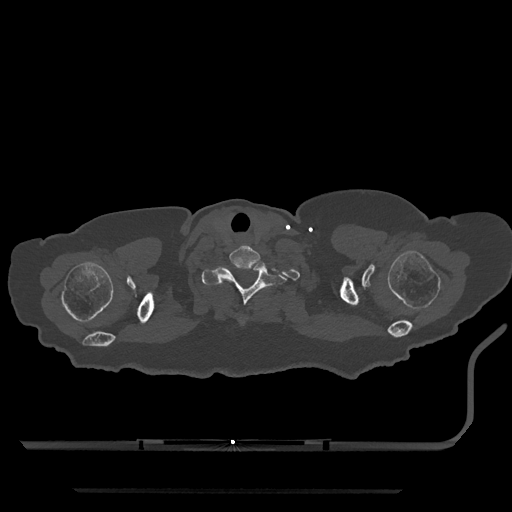
CT including the spine, one axial slice; position 719 of 797 along the scan axis; bone window (W 1800 / L 400 HU); 512 × 512 image matrix. Female patient, age 51 years. From the clinical record (not read from this slice): primary cancer: neuro; vertebrae with lytic lesions (as recorded): T8.
Structures marked on this image (semi-automatically segmented with operator editing):
- T1 vertebra: bounding box (x1, y1, x2, y2) in pixels: (202, 262, 287, 305)